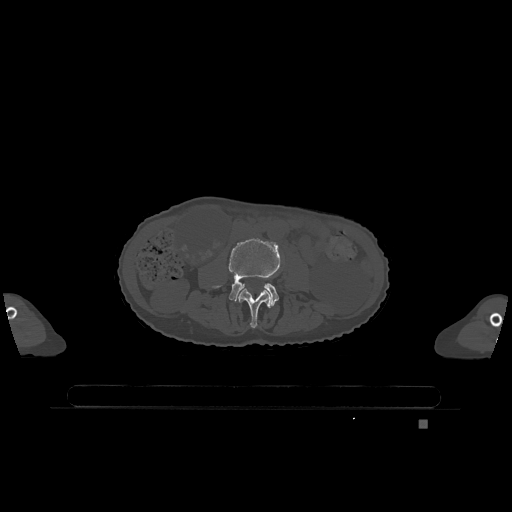
CT including the spine, one axial slice. Slice 326 of 1317 in the series (ordered by position). Bone window (W 1800 / L 400 HU). 0.5 mm slice thickness. 512 × 512 image matrix, field of view 500 × 500 mm. Female patient, age 74 years. Case-level facts recorded for this patient, not image findings: primary cancer: lung; vertebrae with lytic lesions (as recorded): T1, T4, T5, T6, L4, L5.
Annotated regions visible in this slice (semi-automatic segmentation, software-assisted and operator-edited):
- L3 vertebra: bounding box [x1, y1, x2, y2] px = [238, 288, 271, 328]
- L4 vertebra: [213, 238, 280, 306]